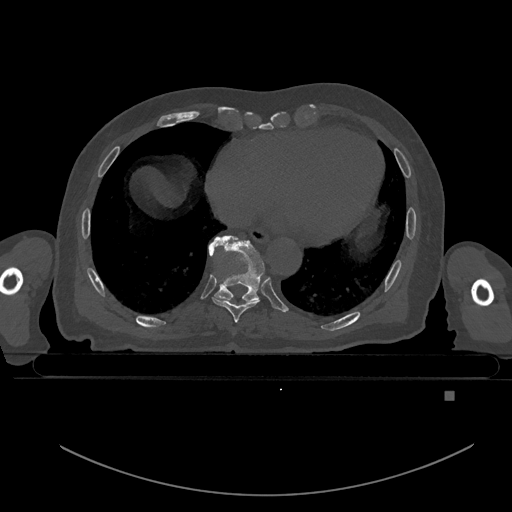
CT including the spine, one axial slice; position 177 of 969 along the scan axis; bone window (W 1800 / L 400 HU); 512 × 512 image matrix, field of view 456 × 456 mm. Patient: male, 82 years. From the clinical record (not read from this slice): primary cancer: prostate; vertebrae with lytic lesions (as recorded): T11, T9, T8, T2.
Structures marked on this image (semi-automatically segmented with operator editing):
- T8 vertebra: bounding box (x1, y1, x2, y2) in pixels: (212, 297, 260, 322)
- T9 vertebra: (208, 235, 265, 303)